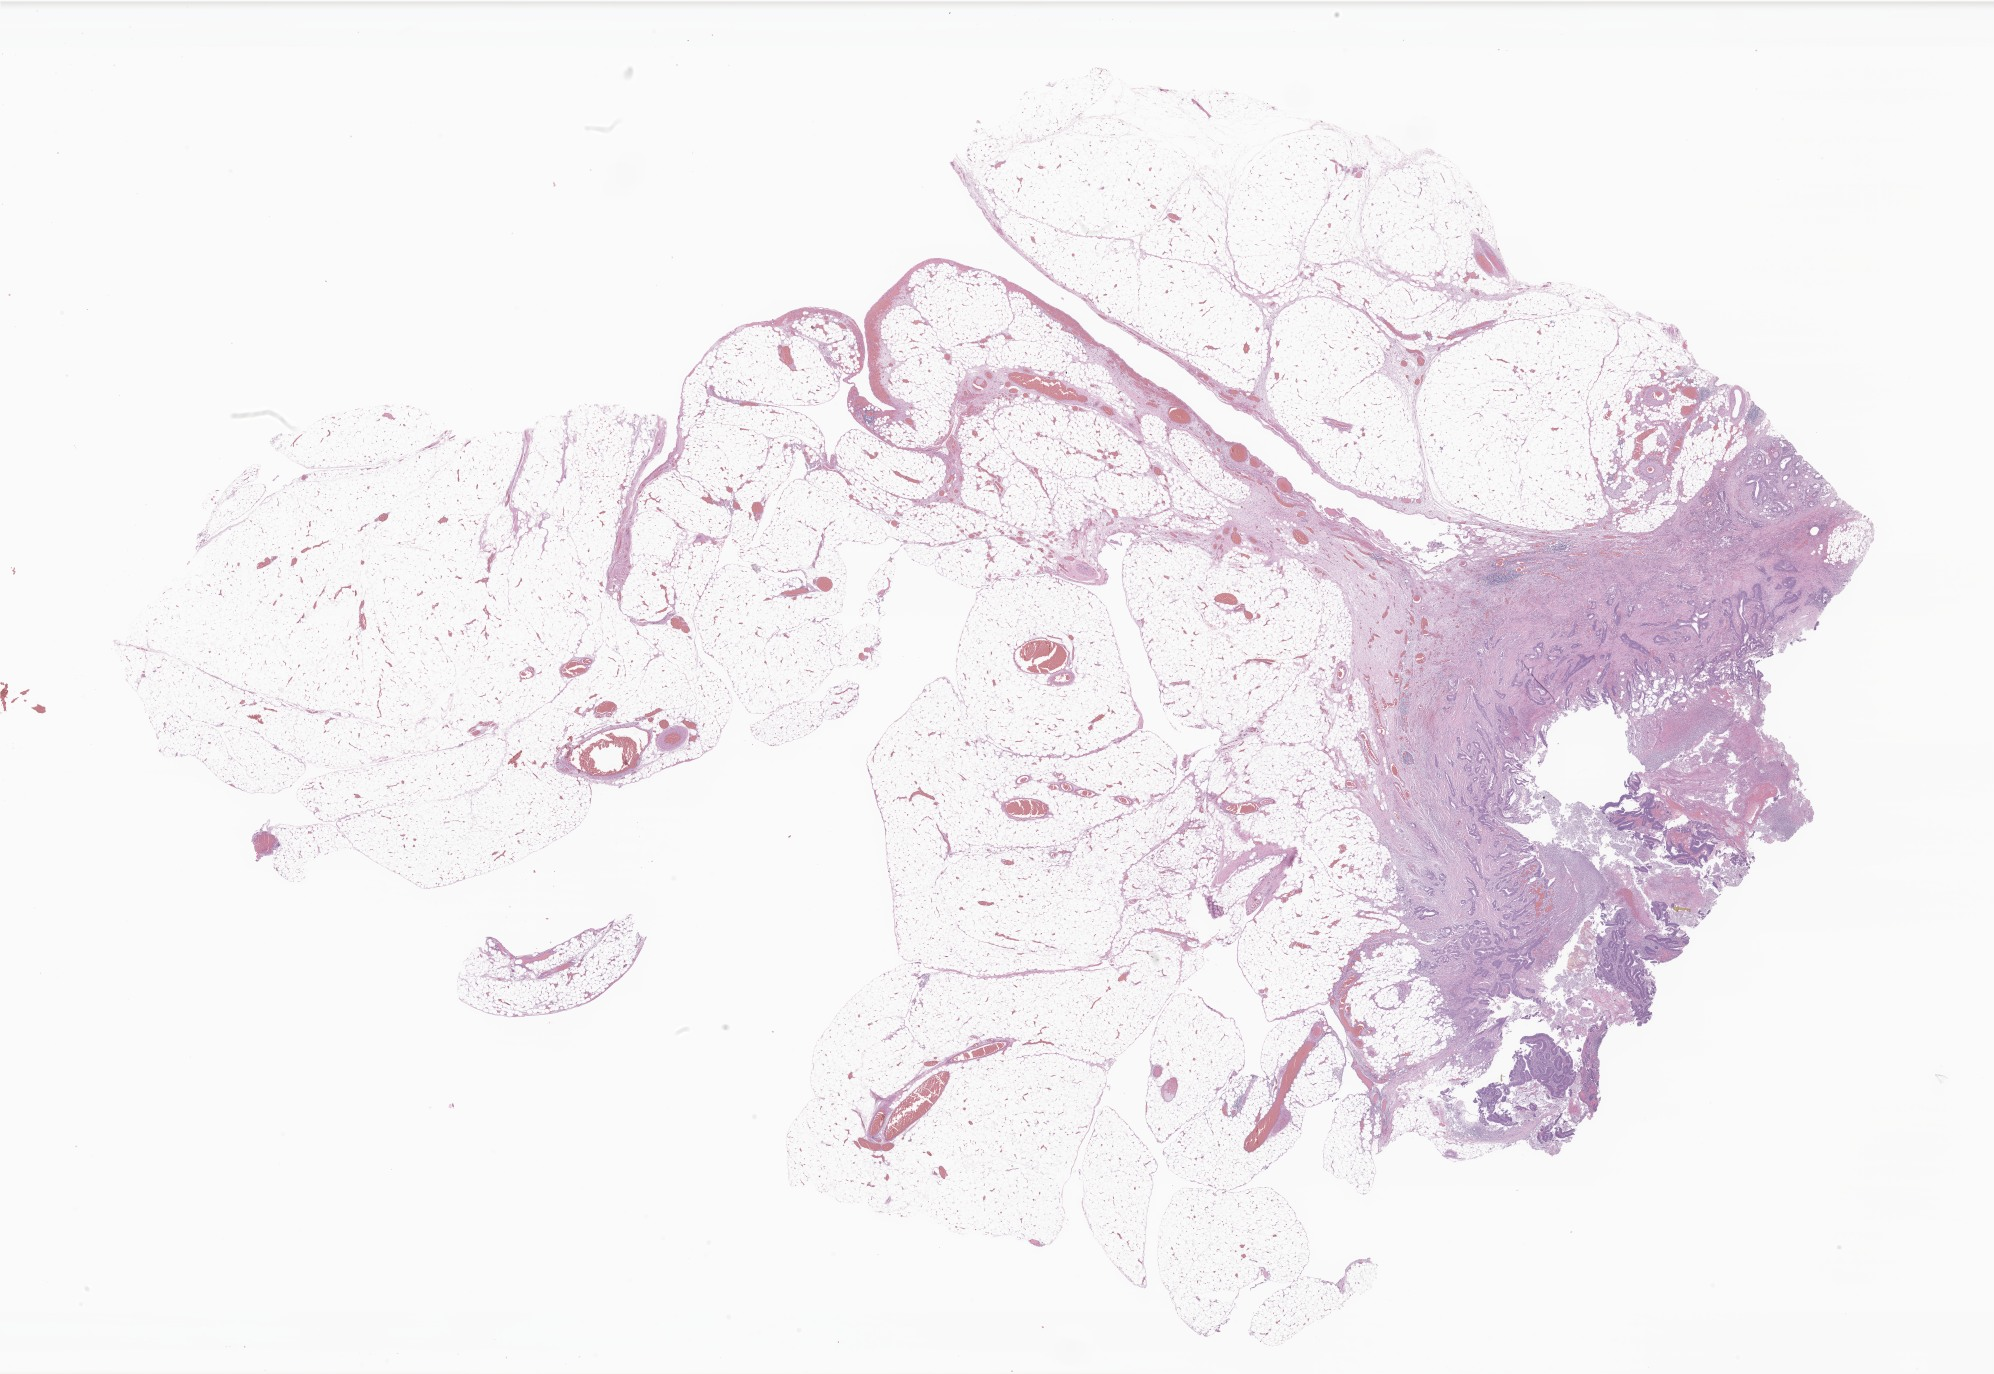
Digitized hematoxylin and eosin (H&E)-stained section of tumor tissue from the colon — shown as a low-resolution overview of the whole scanned area (about 33.6 x 23.2 mm); formalin-fixed, paraffin-embedded (FFPE) tissue. Patient male; age 239 months (19 years 11 months).
* diagnosis (ICD-O-3 morphology term): Adenocarcinoma, NOS